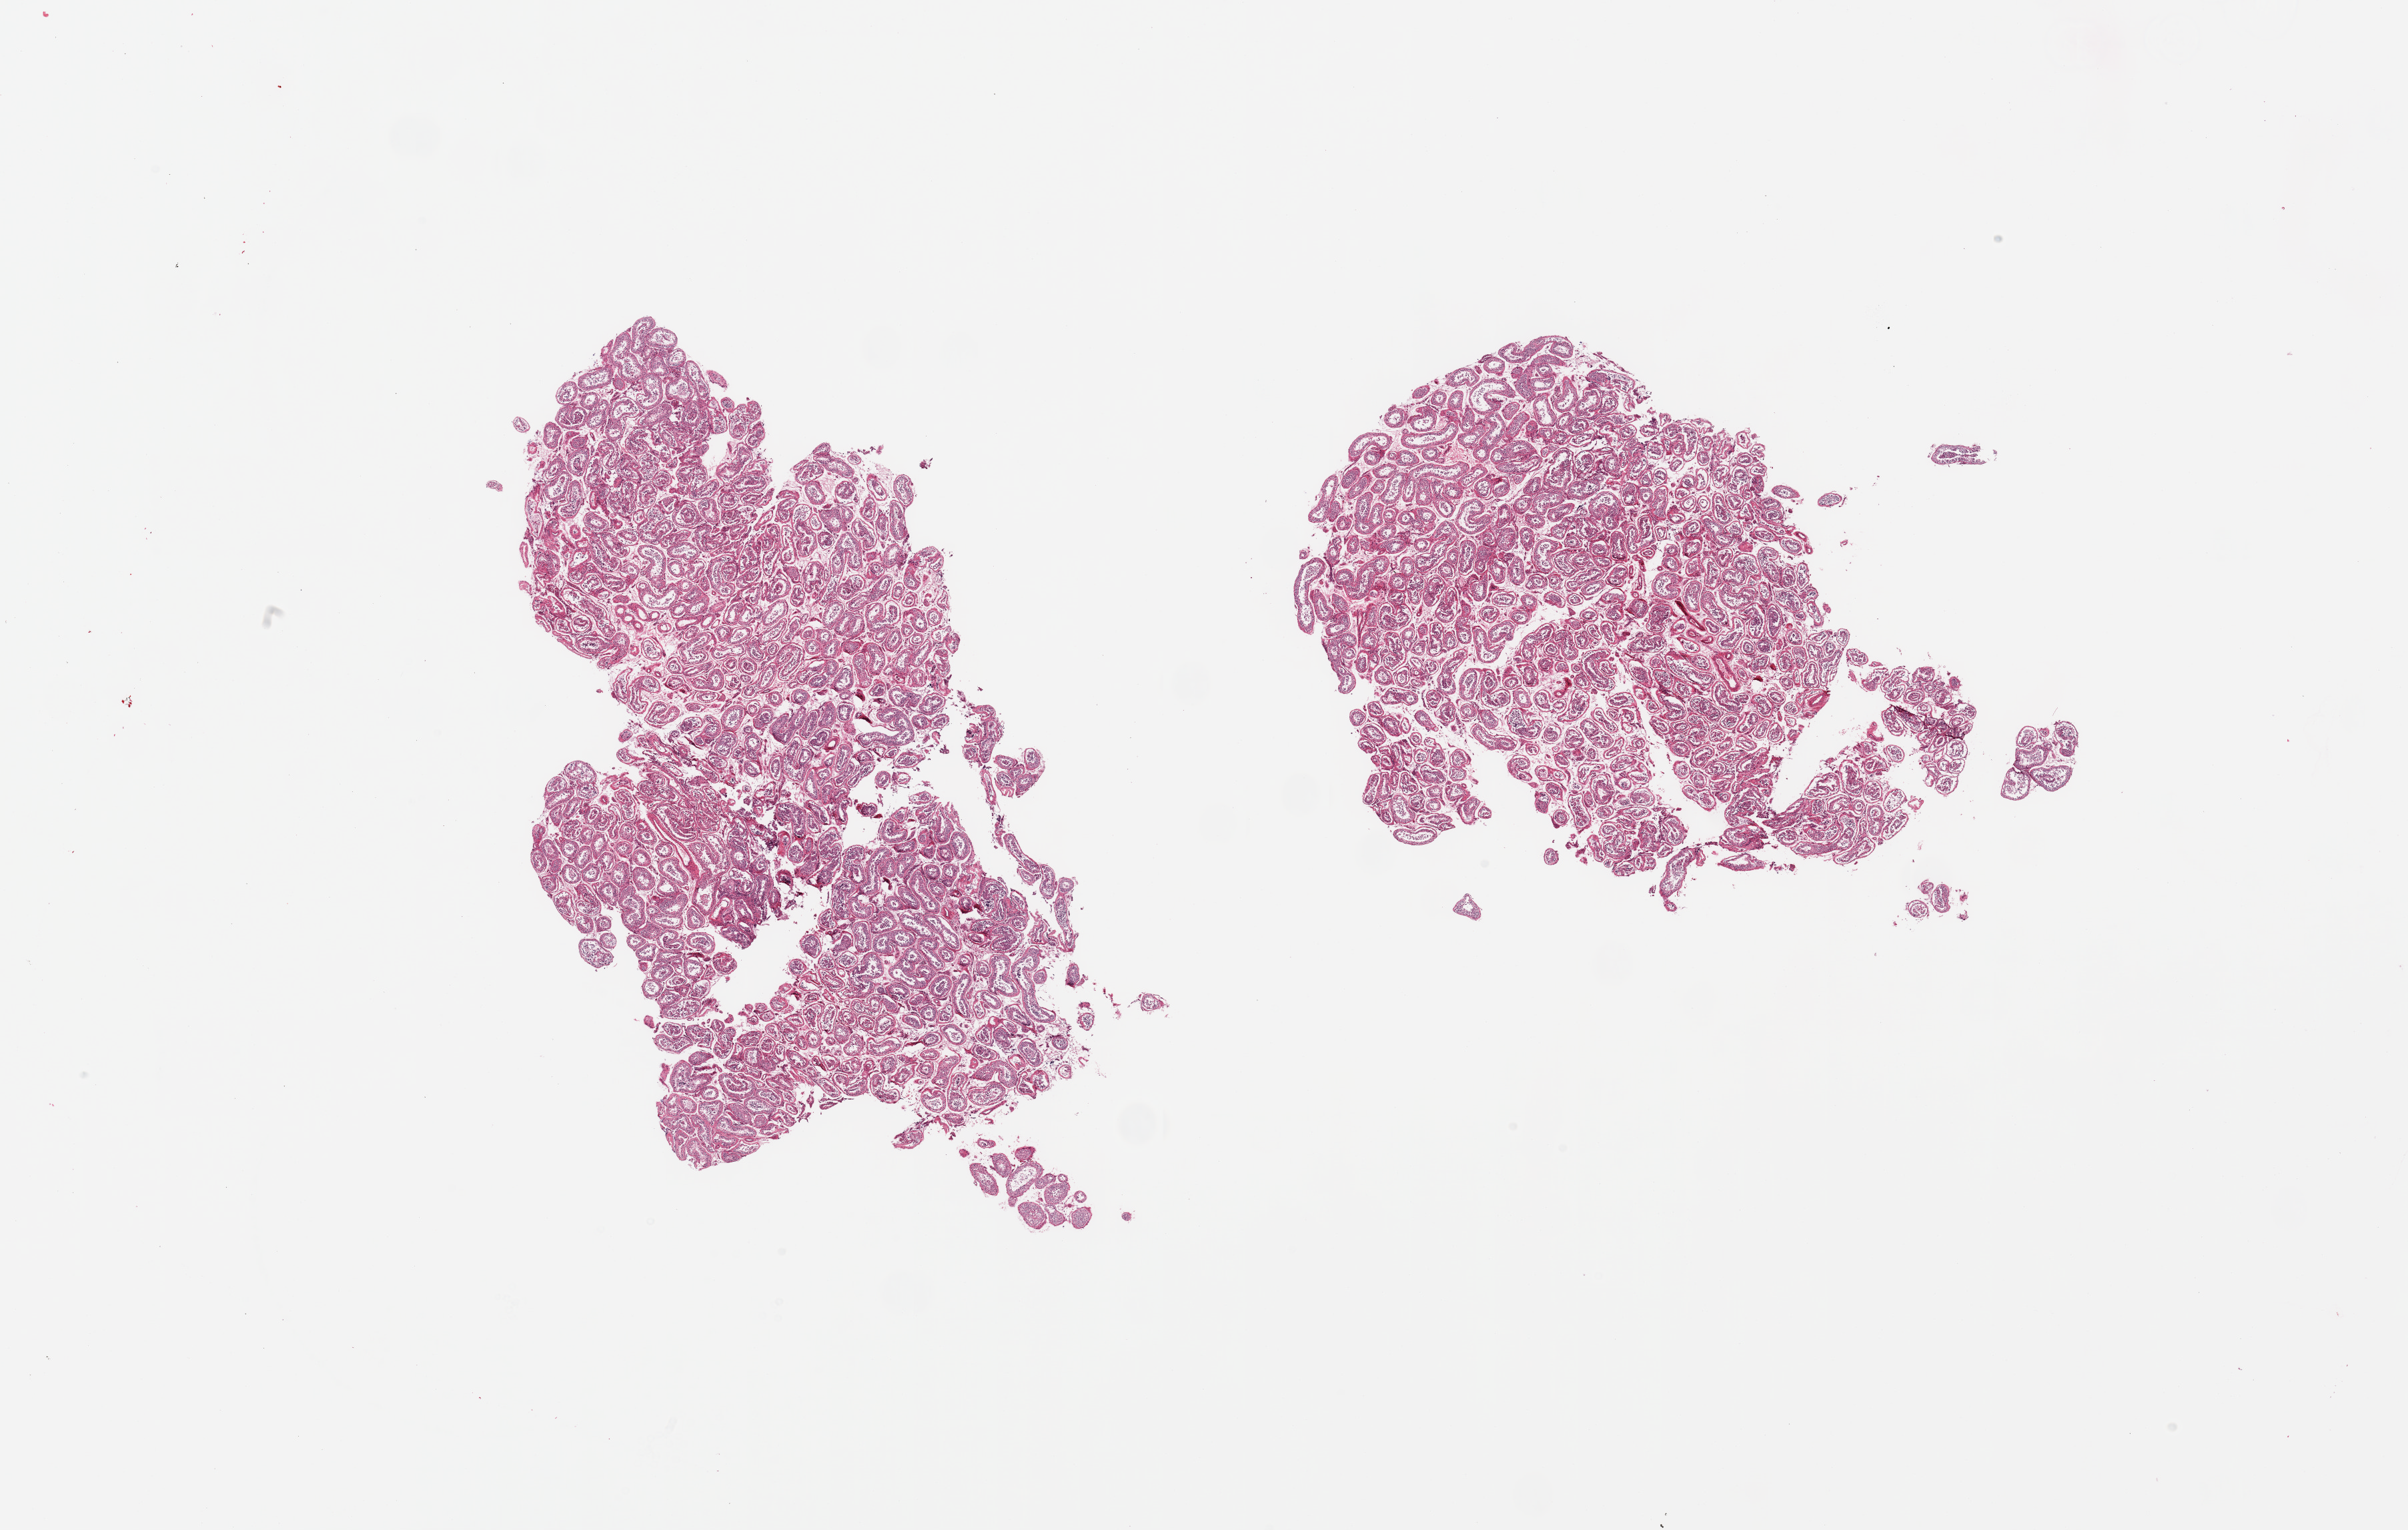
Whole-slide image, H&E stain, low-resolution overview of the scanned area, about 28.5 x 18.1 mm (acquisition: 20x scan). PAXgene-fixed paraffin-embedded (PFPE) section. Sampled site (target tissue): testis. Tissue donor sample.
Pathologist's review note for this sample: 2 pieces; spermatogenesis is present/reduced.